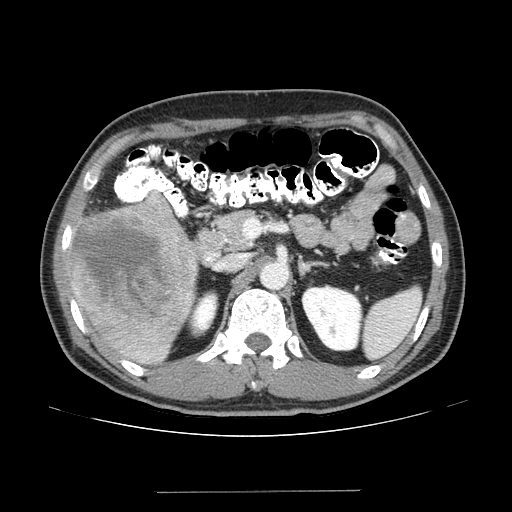
Contrast-enhanced abdominal CT (liver protocol), one axial slice; position 73 of 131 along the scan axis; 100 kVp; one of 2 acquisitions stored at this slice position; soft-tissue window (W 400 / L 40 HU); 2.5 mm slice thickness; 512 × 512 image matrix, field of view 380 × 380 mm. Case-level facts recorded for this patient, not image findings: diagnosis: hepatocellular carcinoma (patient treated with transarterial chemoembolisation; whether this scan precedes or follows treatment is not stated here); TNM stage (as recorded): Stage-I; Child-Pugh class: A; tumour nodularity: uninodular; tumour size: 10.3 cm.
Structures marked on this image (semi-automatic segmentation, software-assisted and operator-edited):
- liver parenchyma outside the tumour (the mass and vessels are separate outlines, so this box may not span the whole liver): bounding box (x1, y1, x2, y2) in pixels: (66, 194, 198, 364)
- mass: (72, 195, 196, 327)